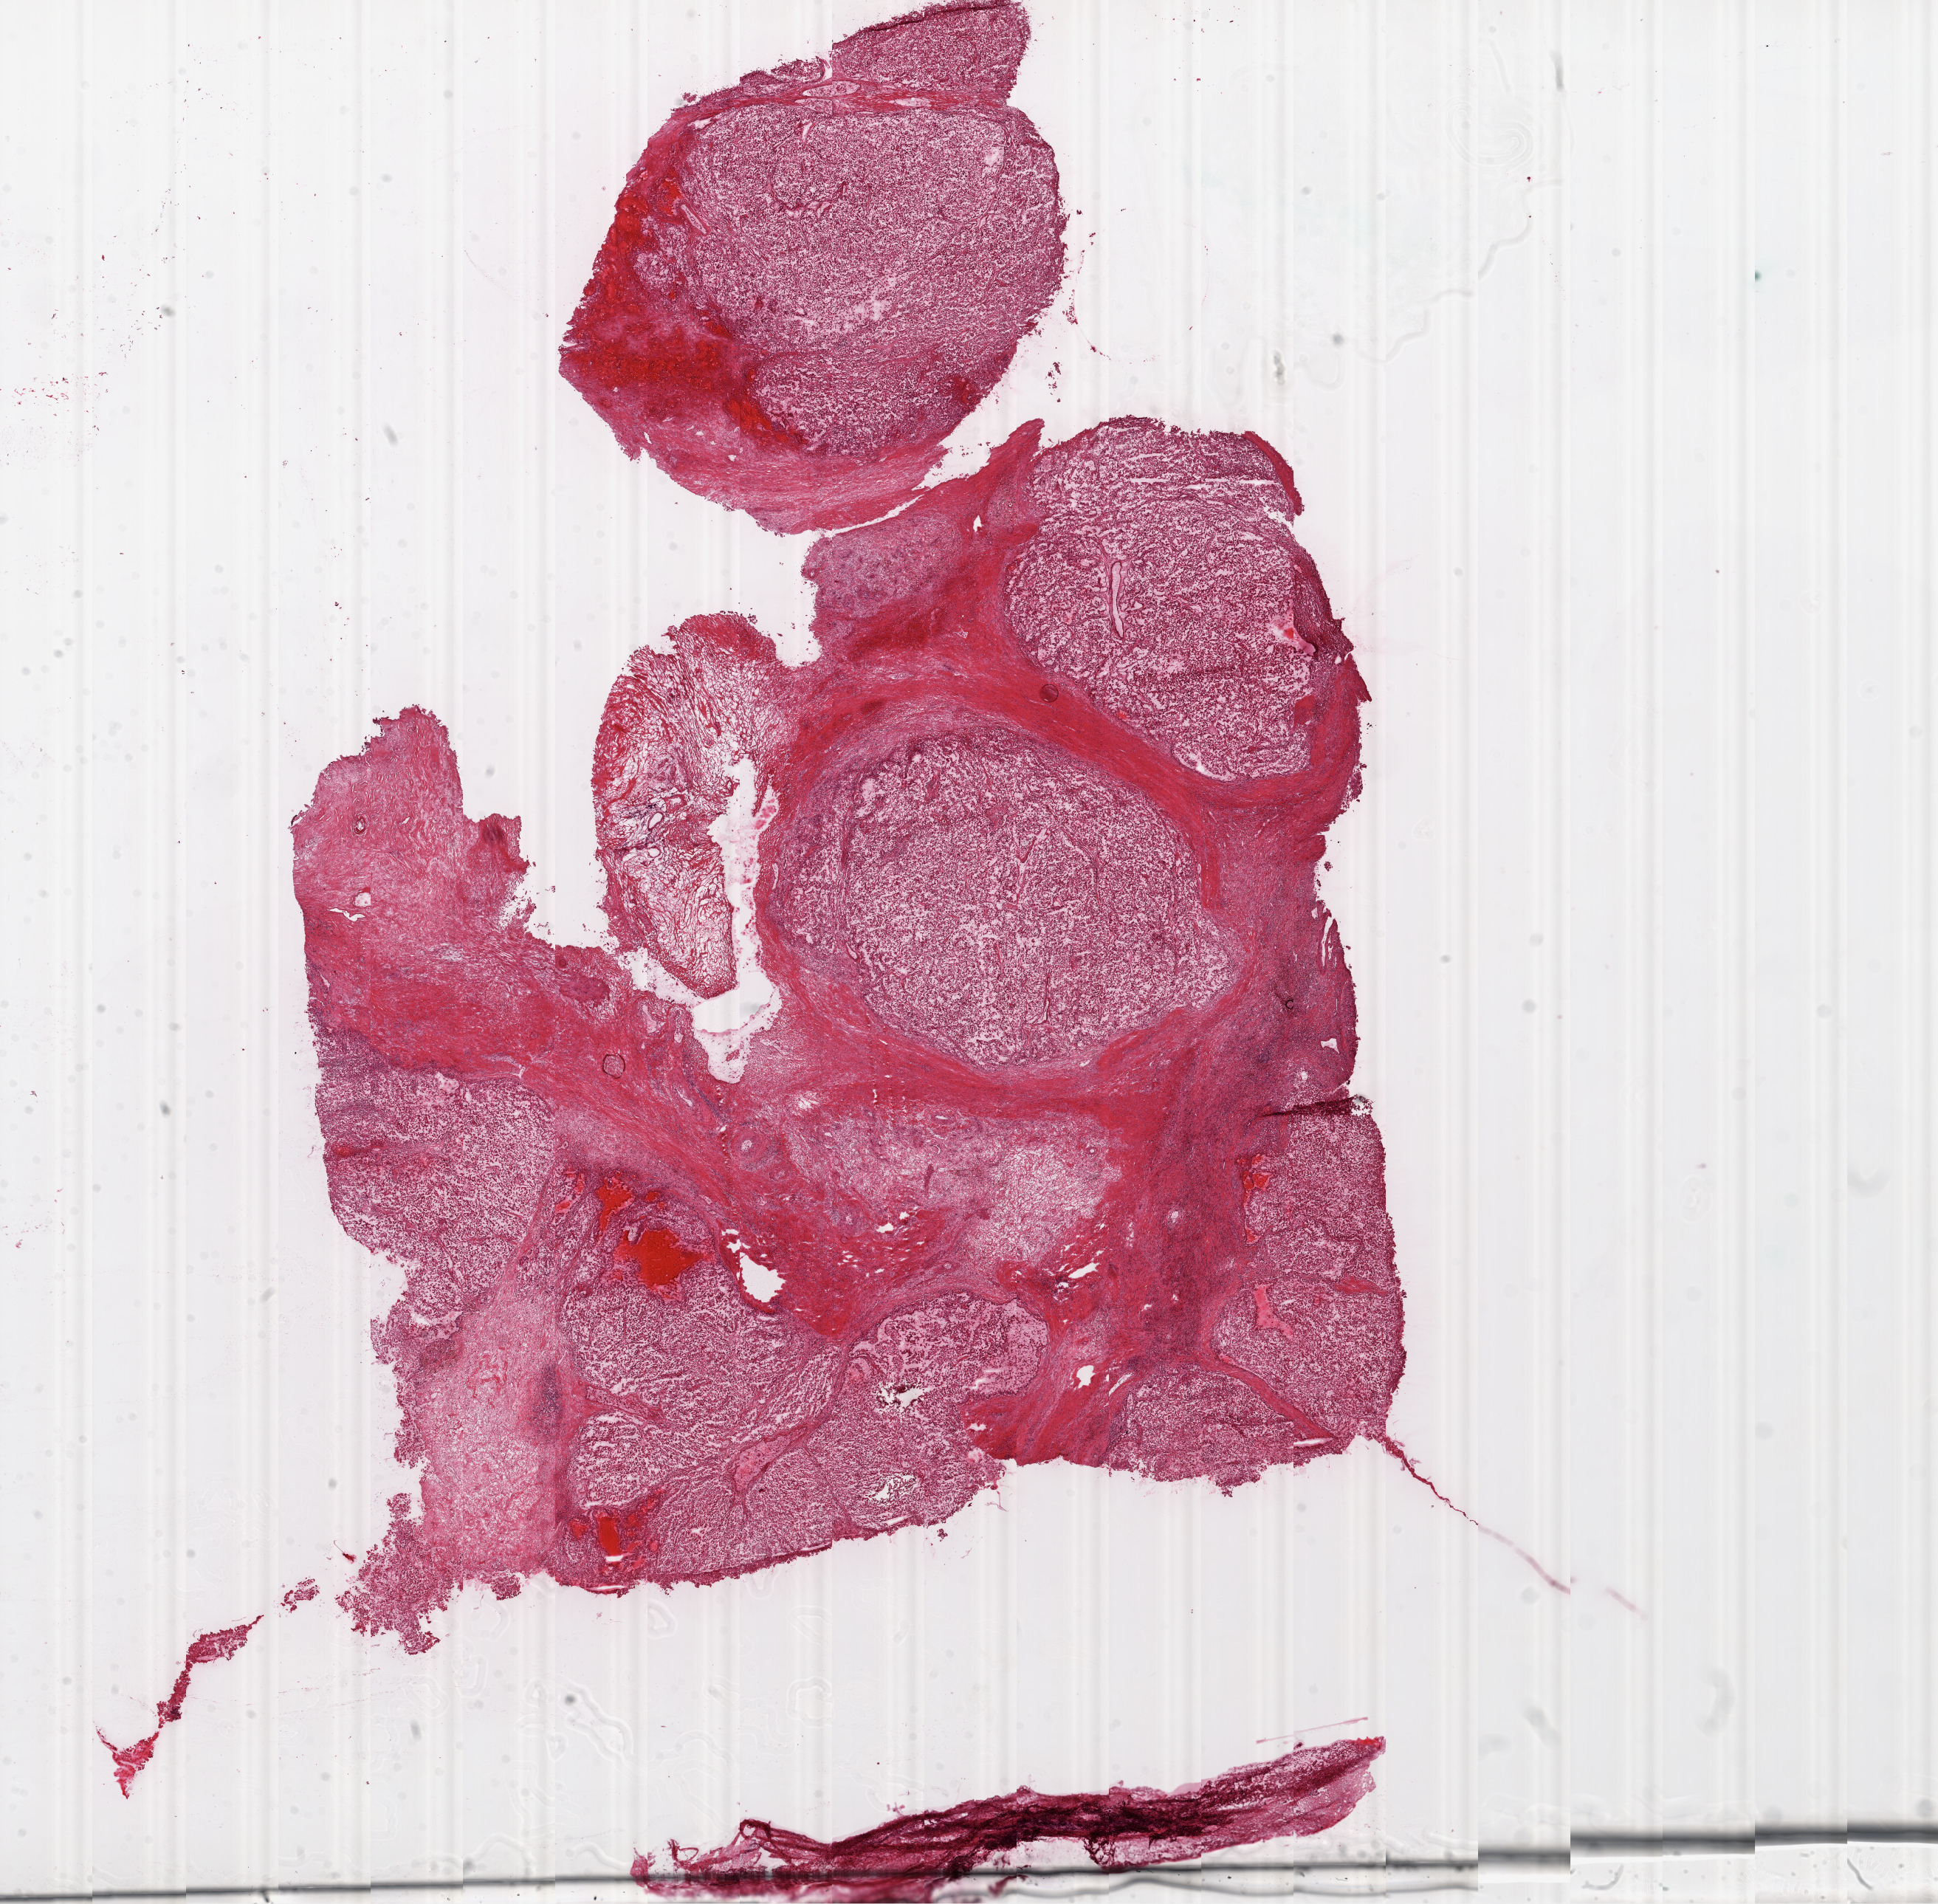
Hematoxylin and eosin (H&E) stained whole-slide image, shown as a low-resolution overview of the whole scanned area (about 21.1 x 20.7 mm). Frozen section. Kidney, primary tumour sample. Male, age 58 years at initial diagnosis. Histologic grade: G2 (moderately differentiated). Slide review estimates, as recorded: tumour cells 75%, tumour nuclei 80%, normal cells 0%, stromal cells 25%, necrosis 0%.
- diagnosis: Clear cell adenocarcinoma, NOS
- AJCC pathologic stage: II